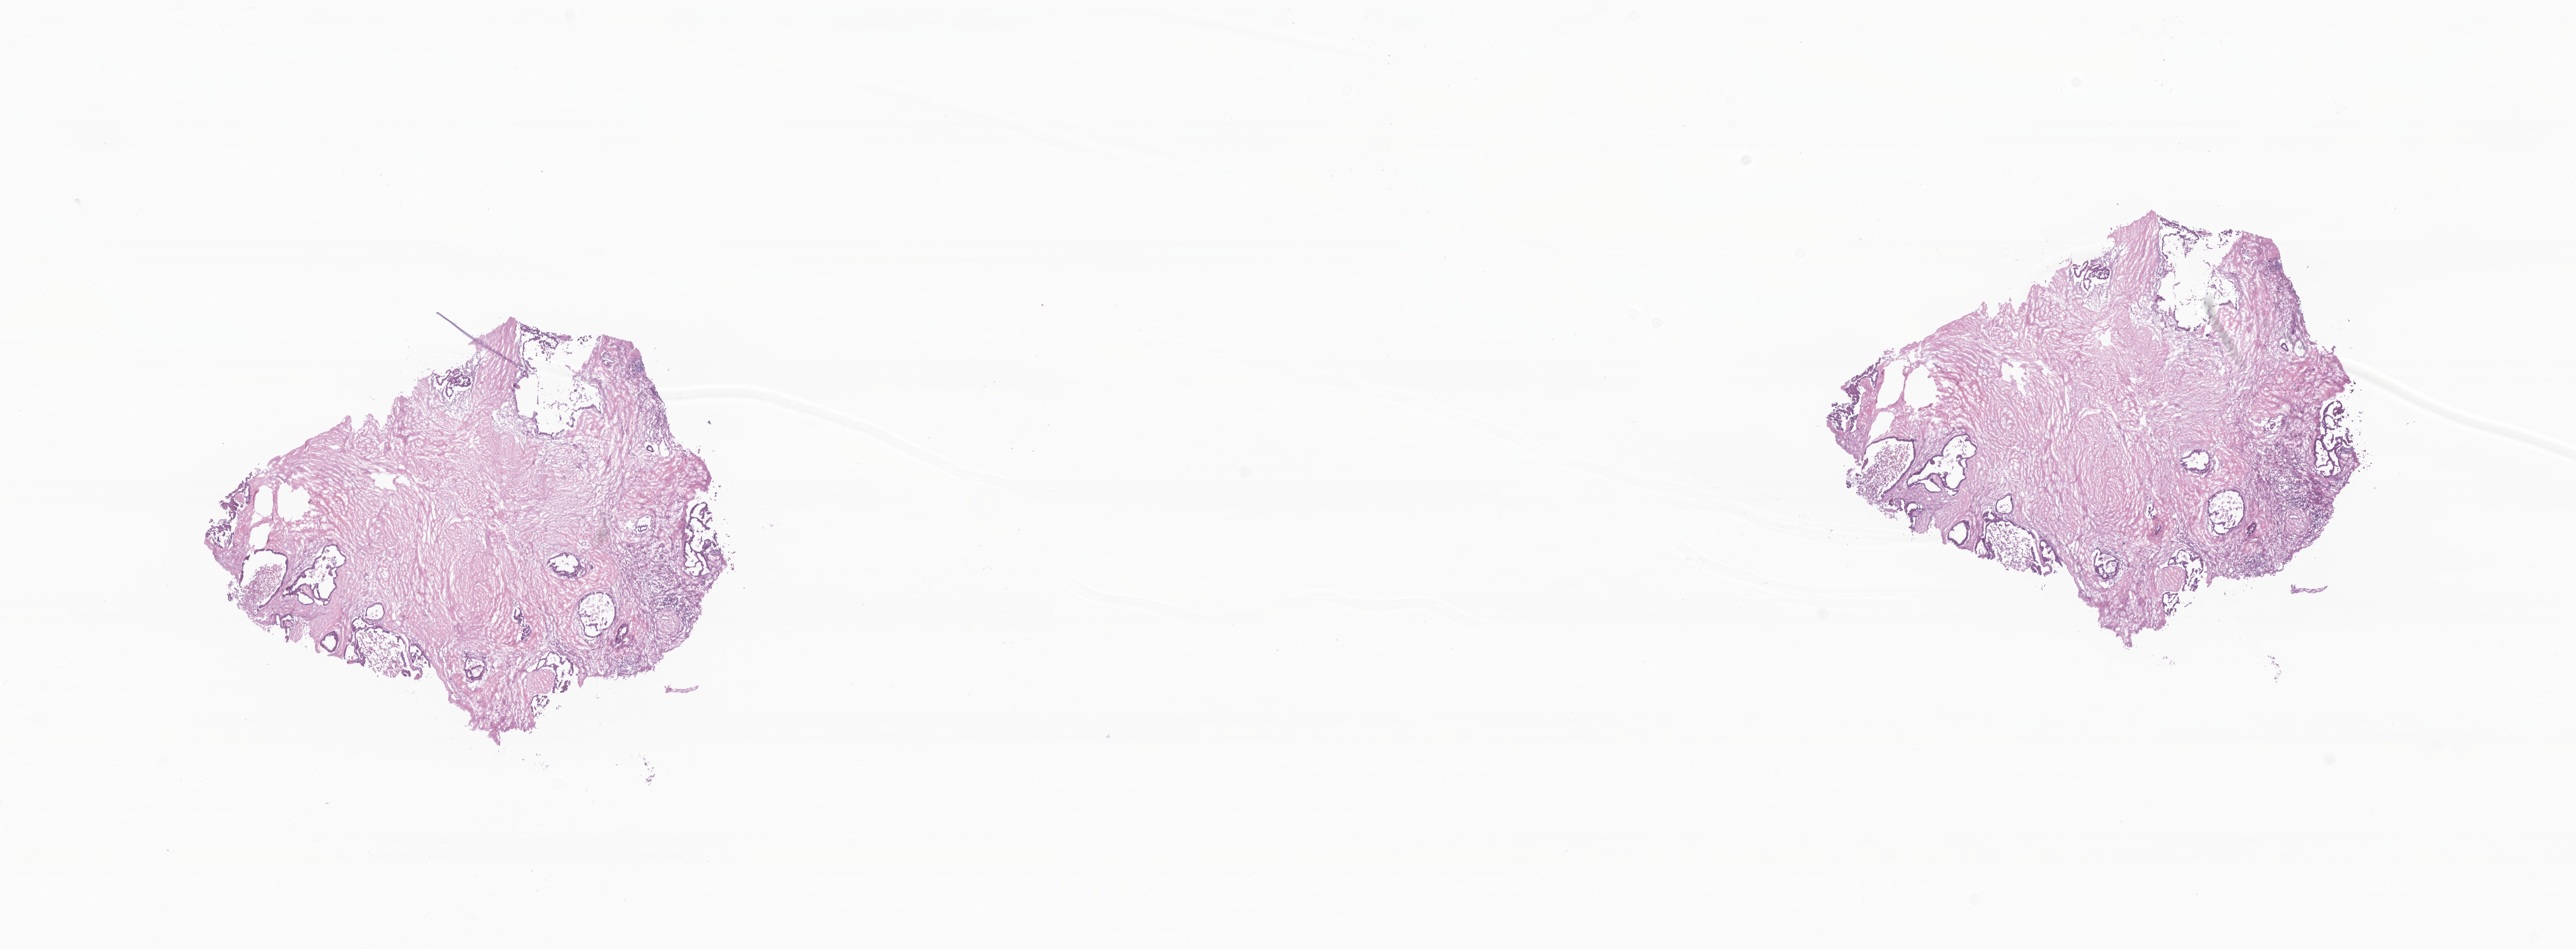
Whole-slide image, H&E stain, shown as a low-resolution overview of the whole scanned area (about 23.1 x 8.5 mm); frozen section; metastatic tumor tissue, resected from liver. Male, age 70 years at initial diagnosis. Slide review estimates, as recorded: tumor cells 80%, tumor nuclei 80%, stromal cells 17%, necrosis 3%, normal cells 0%. Inflammatory infiltration, as recorded: lymphocyte infiltration 4%, monocyte infiltration 2%, neutrophil infiltration 8%.
Section: bottom of the tissue portion. Patient diagnosis (primary): Adenocarcinoma, NOS.